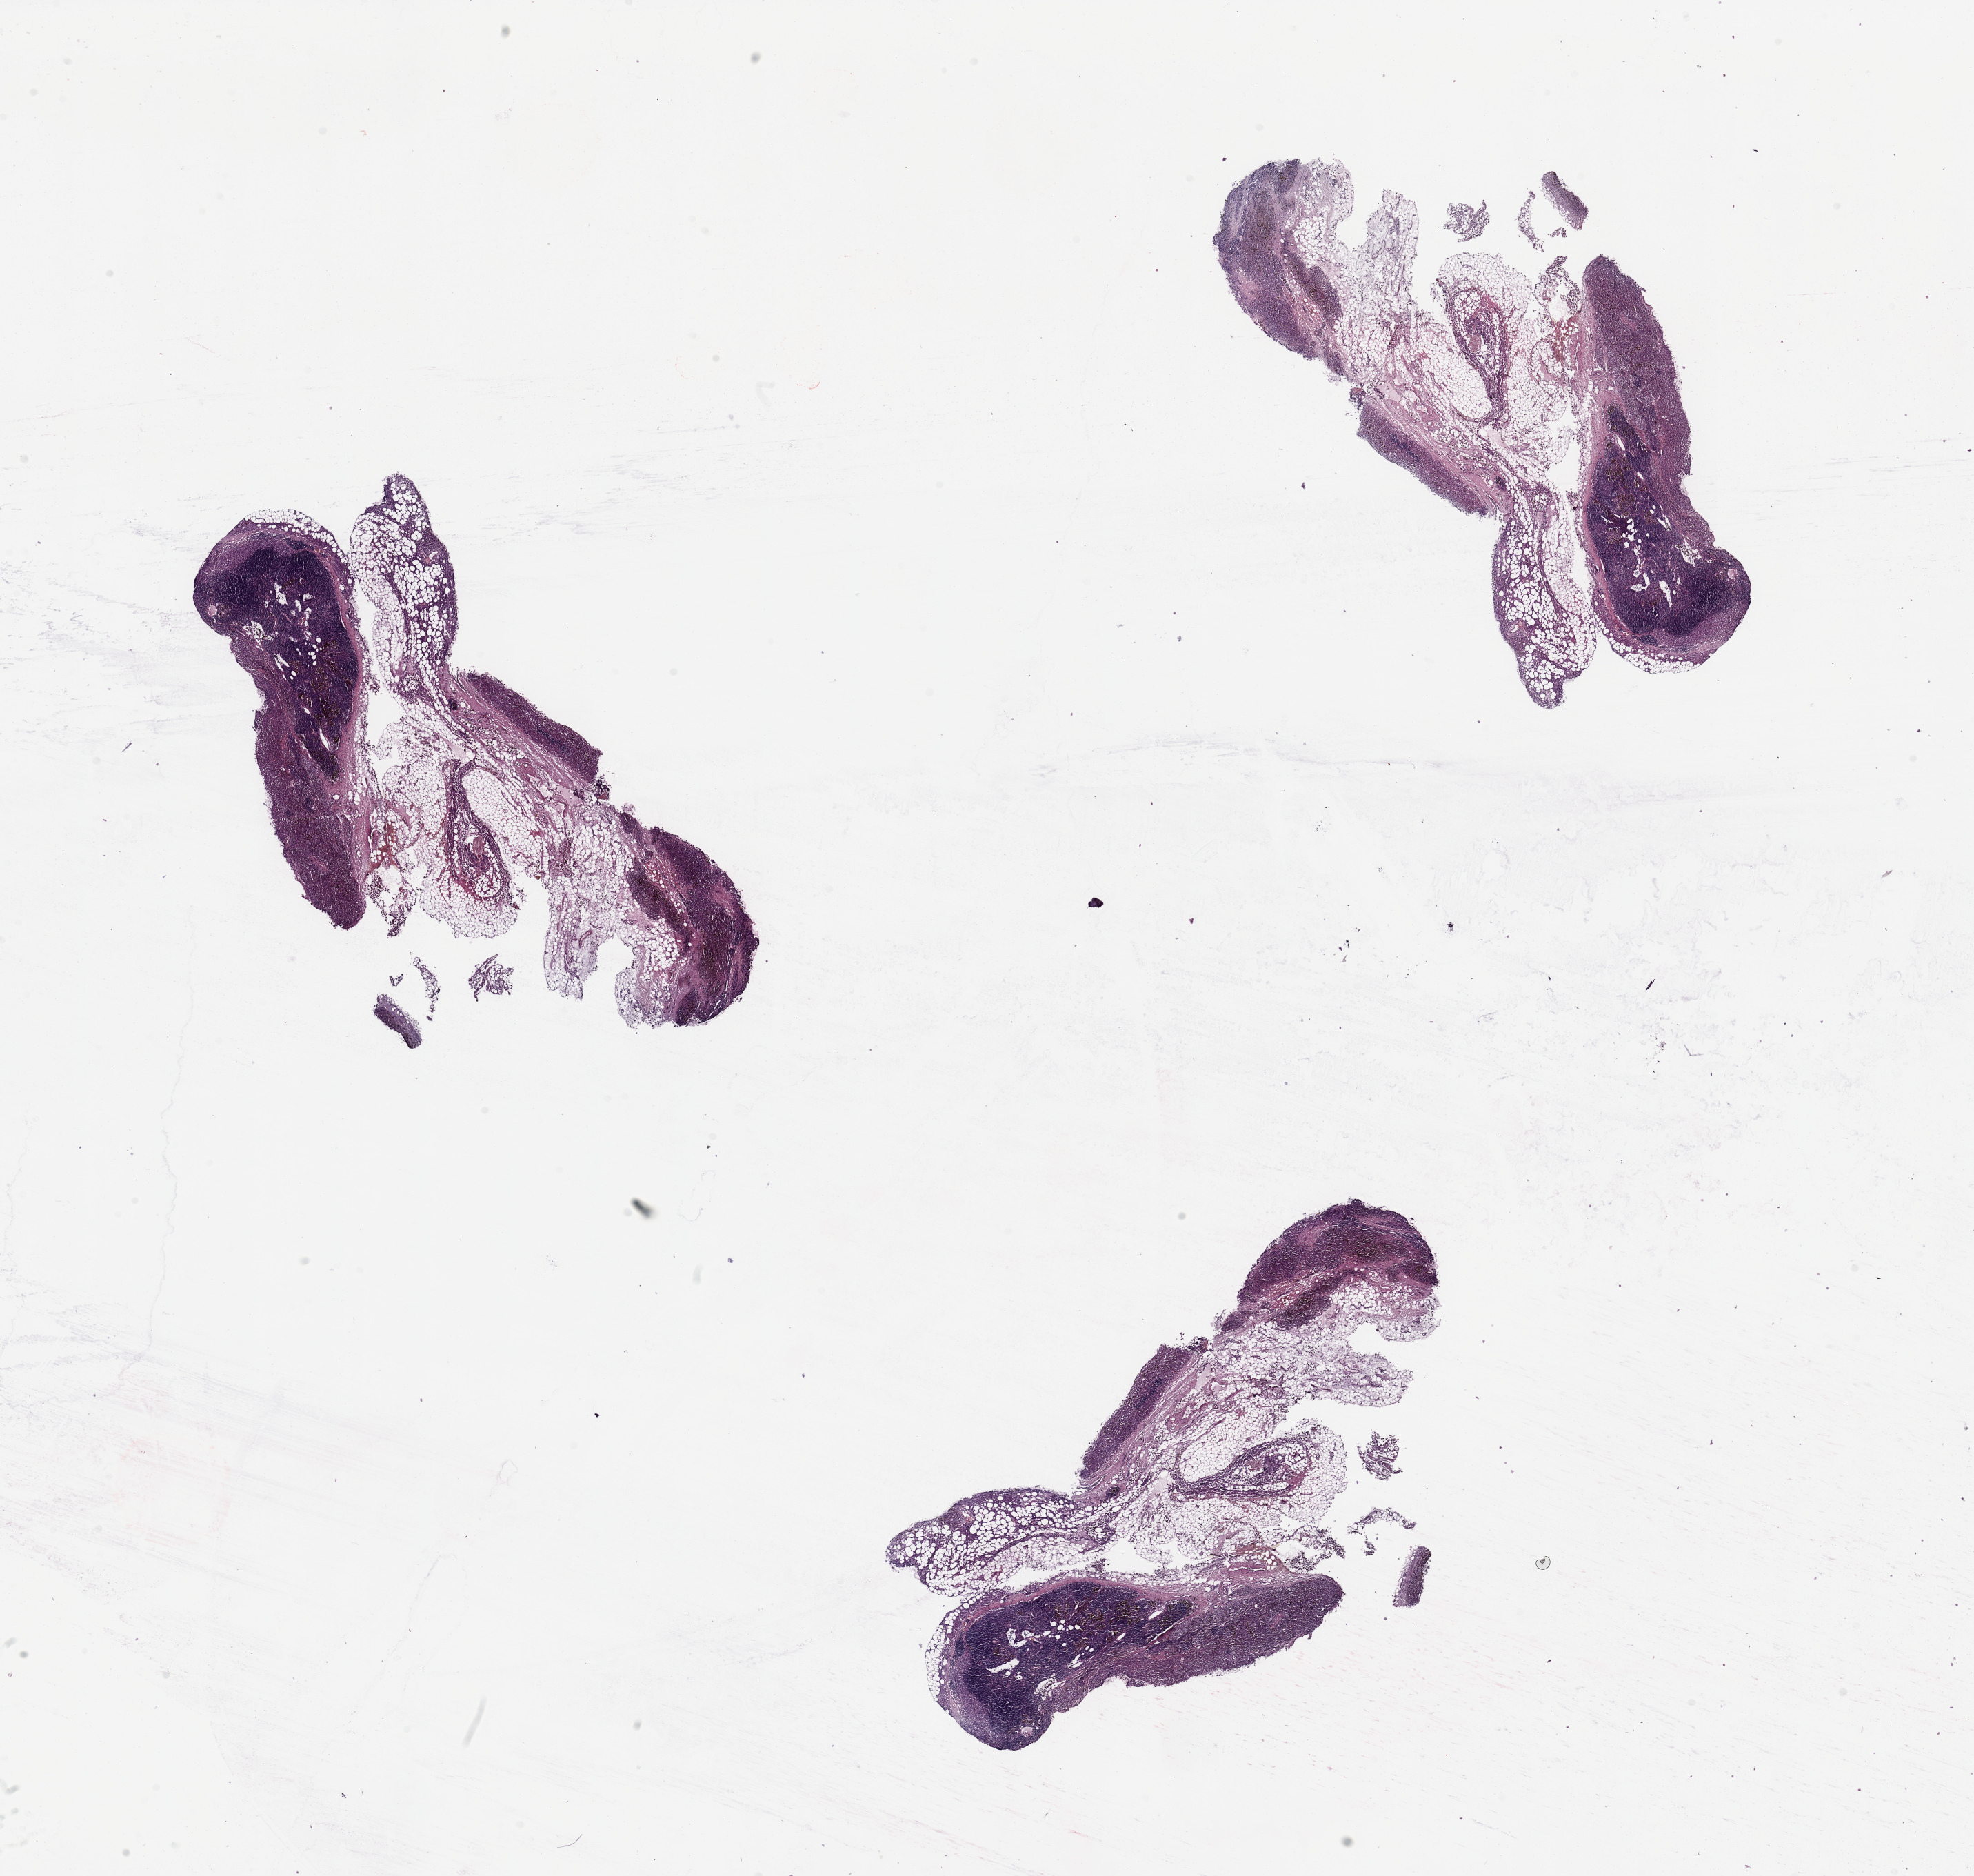
Whole-slide histology image, H&E-stained, a low-resolution overview of the entire scanned area, about 22.6 x 21.5 mm; melanoma tumour tissue; sampled site not recorded. 51-year-old female patient.
AJCC pathologic stage: IB. Primary tumour site (as recorded): trunk. Histologic diagnosis: Malignant melanoma, NOS.